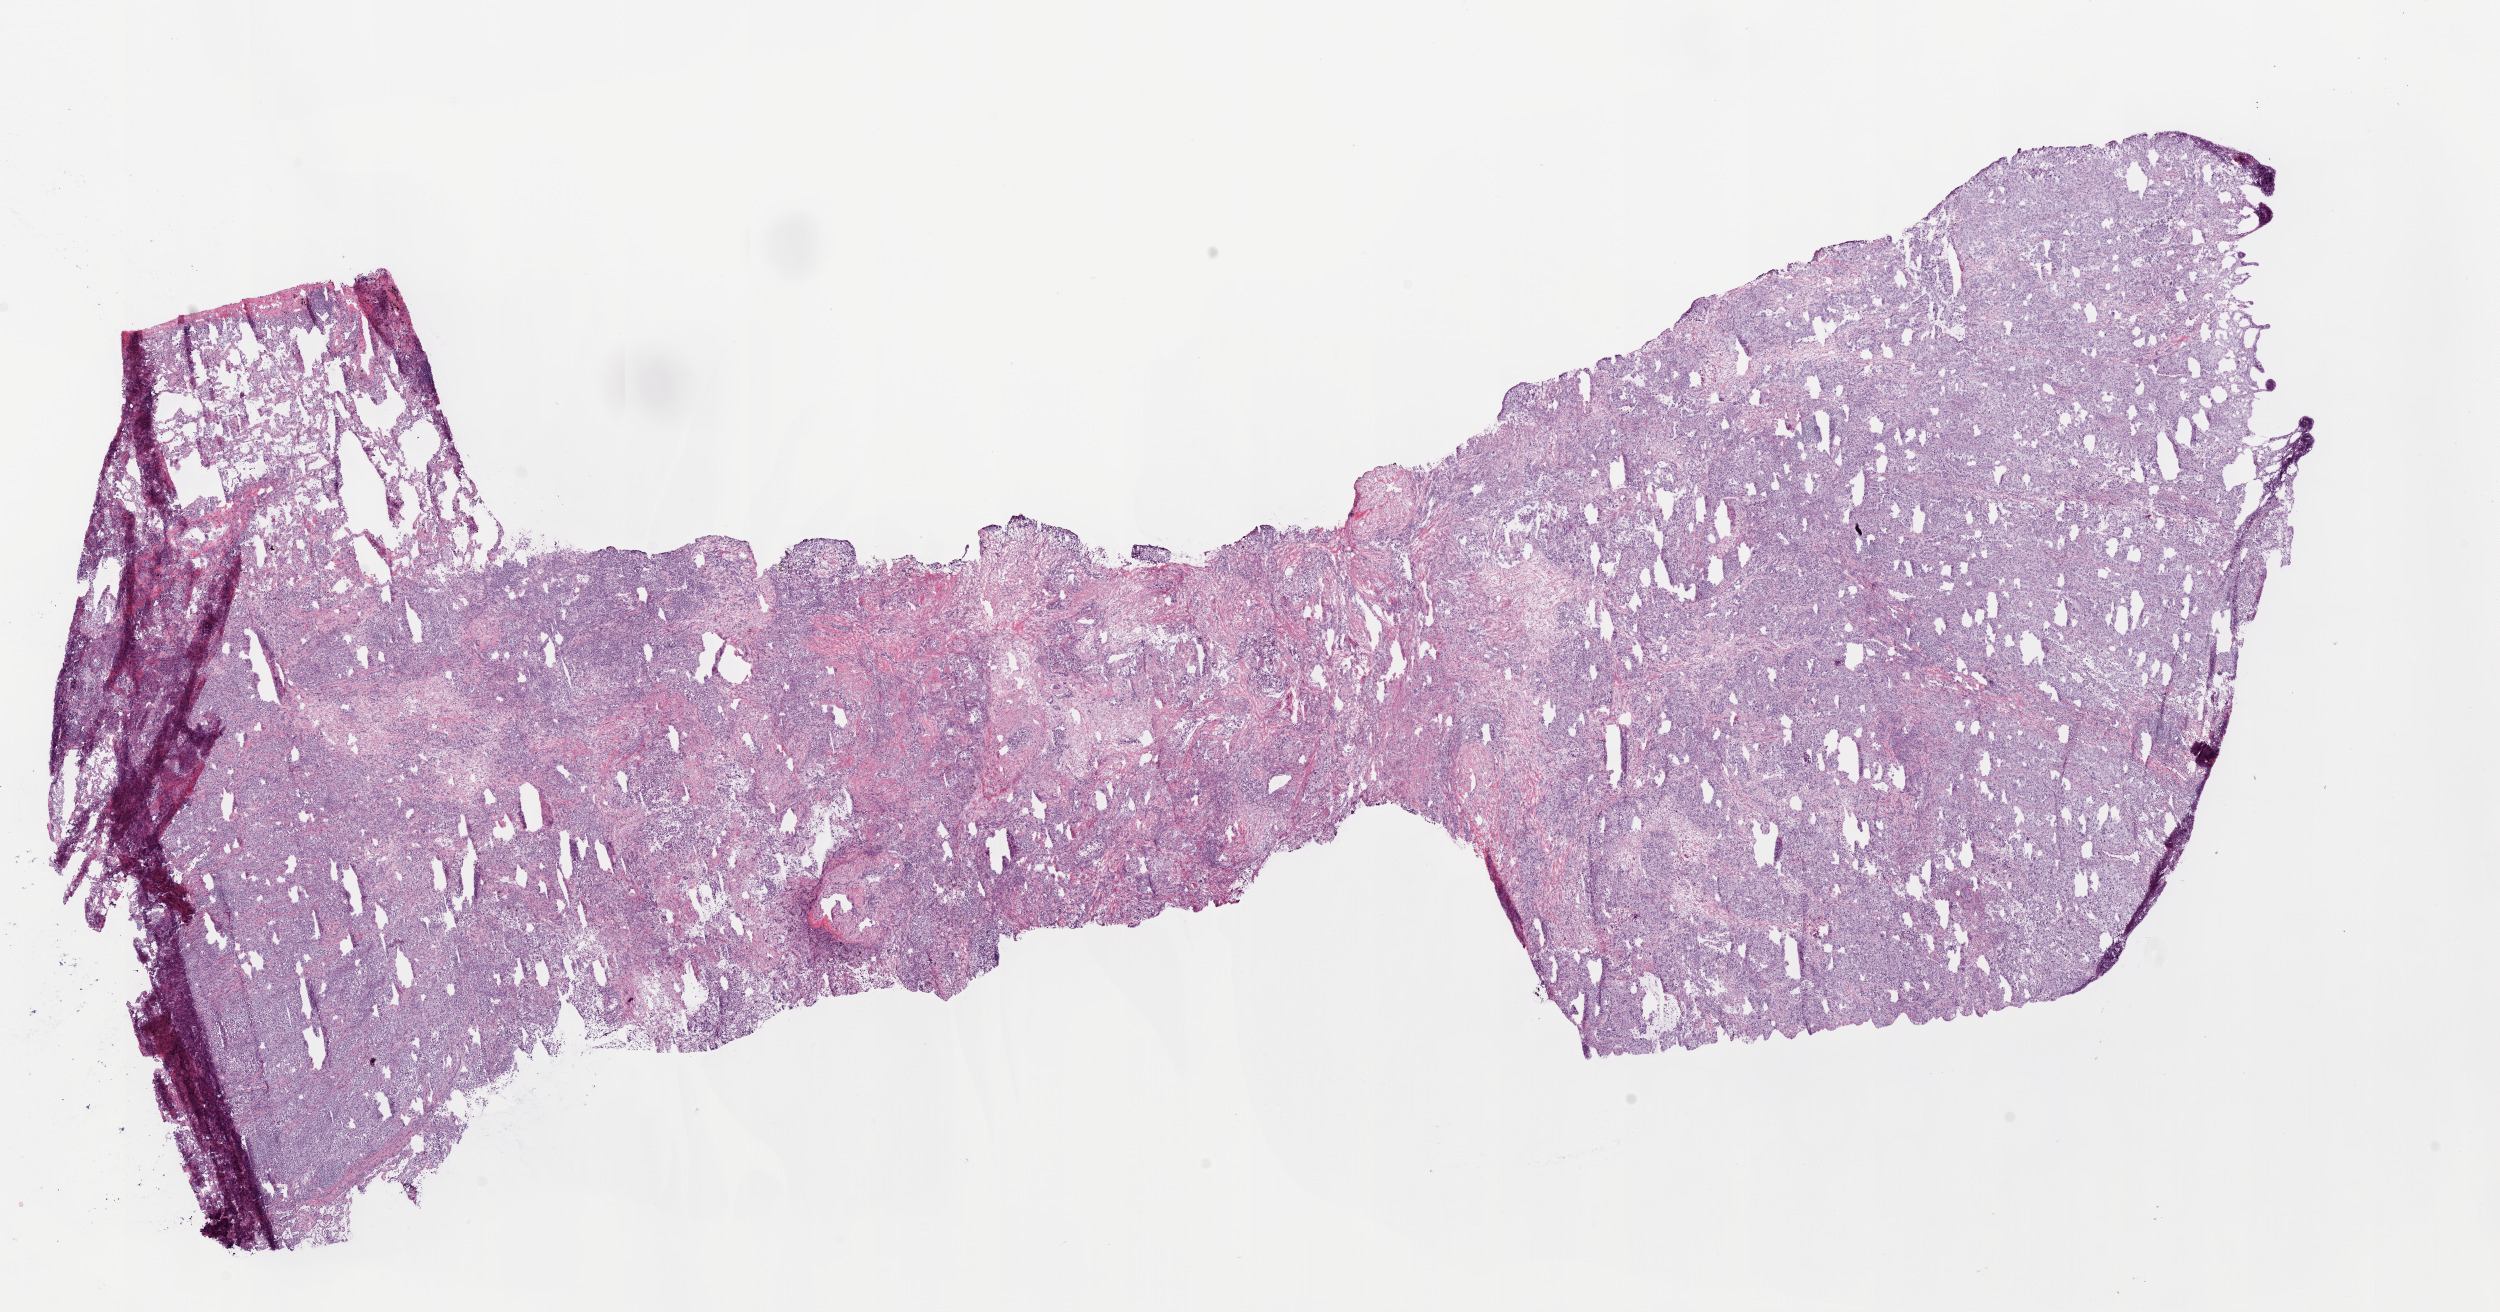
Digitized H&E tissue section (whole slide) — low-resolution overview of the scanned area, about 20.1 x 10.5 mm (slide scanned at 20x); frozen section from the bottom of the tissue portion; primary tumour sample from the lung. Patient: female, age at initial diagnosis 60 years.
Diagnosis: Adenocarcinoma, NOS (upper lobe, lung).